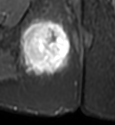
MRI of an extremity soft-tissue mass, one axial slice. Slice 25 of 49 in the series (ordered by position). STIR. MR volume resampled by the dataset authors to the PET/CT grid (not the native acquisition matrix). 115 × 125 image matrix, field of view 112 × 122 mm. Female patient. From the clinical record (not read from this slice): histological type: epithelioid sarcoma; grade: intermediate; site of the primary tumour: right buttock.
Structures marked on this image (expert contour drawn on MRI and transferred to this co-registered scan by the dataset authors):
- gross tumour volume including surrounding oedema: bounding box <17,16,71,76> (left, top, right, bottom; pixels)
- gross tumour volume (mass): <22,21,71,70>